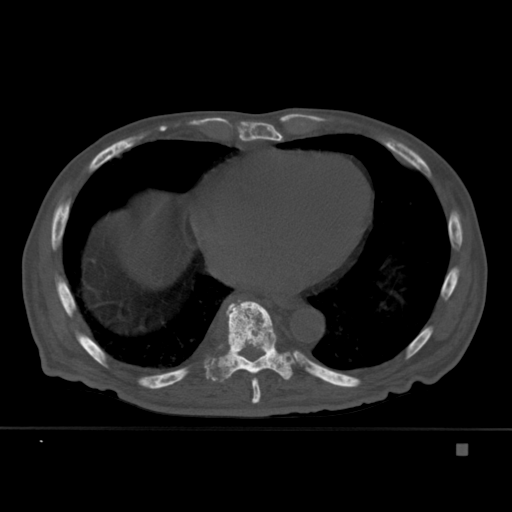
CT including the spine, one axial slice; bone window (W 1800 / L 400 HU); 1.5 mm slice thickness; 512 × 512 image matrix, field of view 378 × 378 mm. Patient: male, 75 years. Case-level facts recorded for this patient, not image findings: primary cancer: prostate.
Structures marked on this image (semi-automatically segmented with operator editing):
- T10 vertebra: bounding box [x1, y1, x2, y2] px = [241, 355, 264, 356]
- T8 vertebra: [243, 369, 261, 404]
- T9 vertebra: [205, 300, 295, 382]